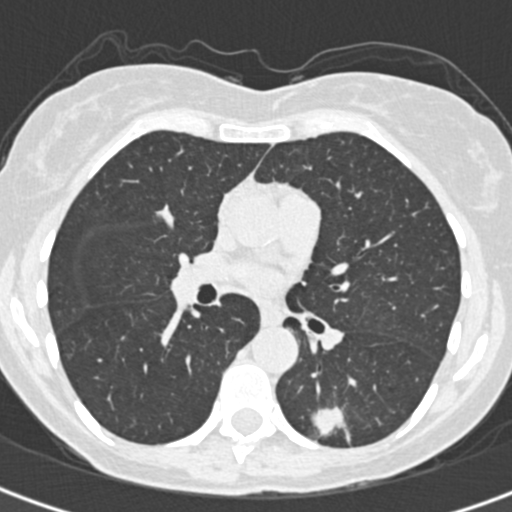
Low-dose screening chest CT, one axial slice; reconstruction kernel B30f; 120 kVp; lung window (W 1500 / L -600 HU); 1 mm slice thickness; 512 × 512 image matrix.
Outlined on this slice (outlined manually by an expert reader):
- lesion 1 (tumor, lower lobe of left lung): bounding box (x1, y1, x2, y2) in pixels: (312, 407, 346, 436)